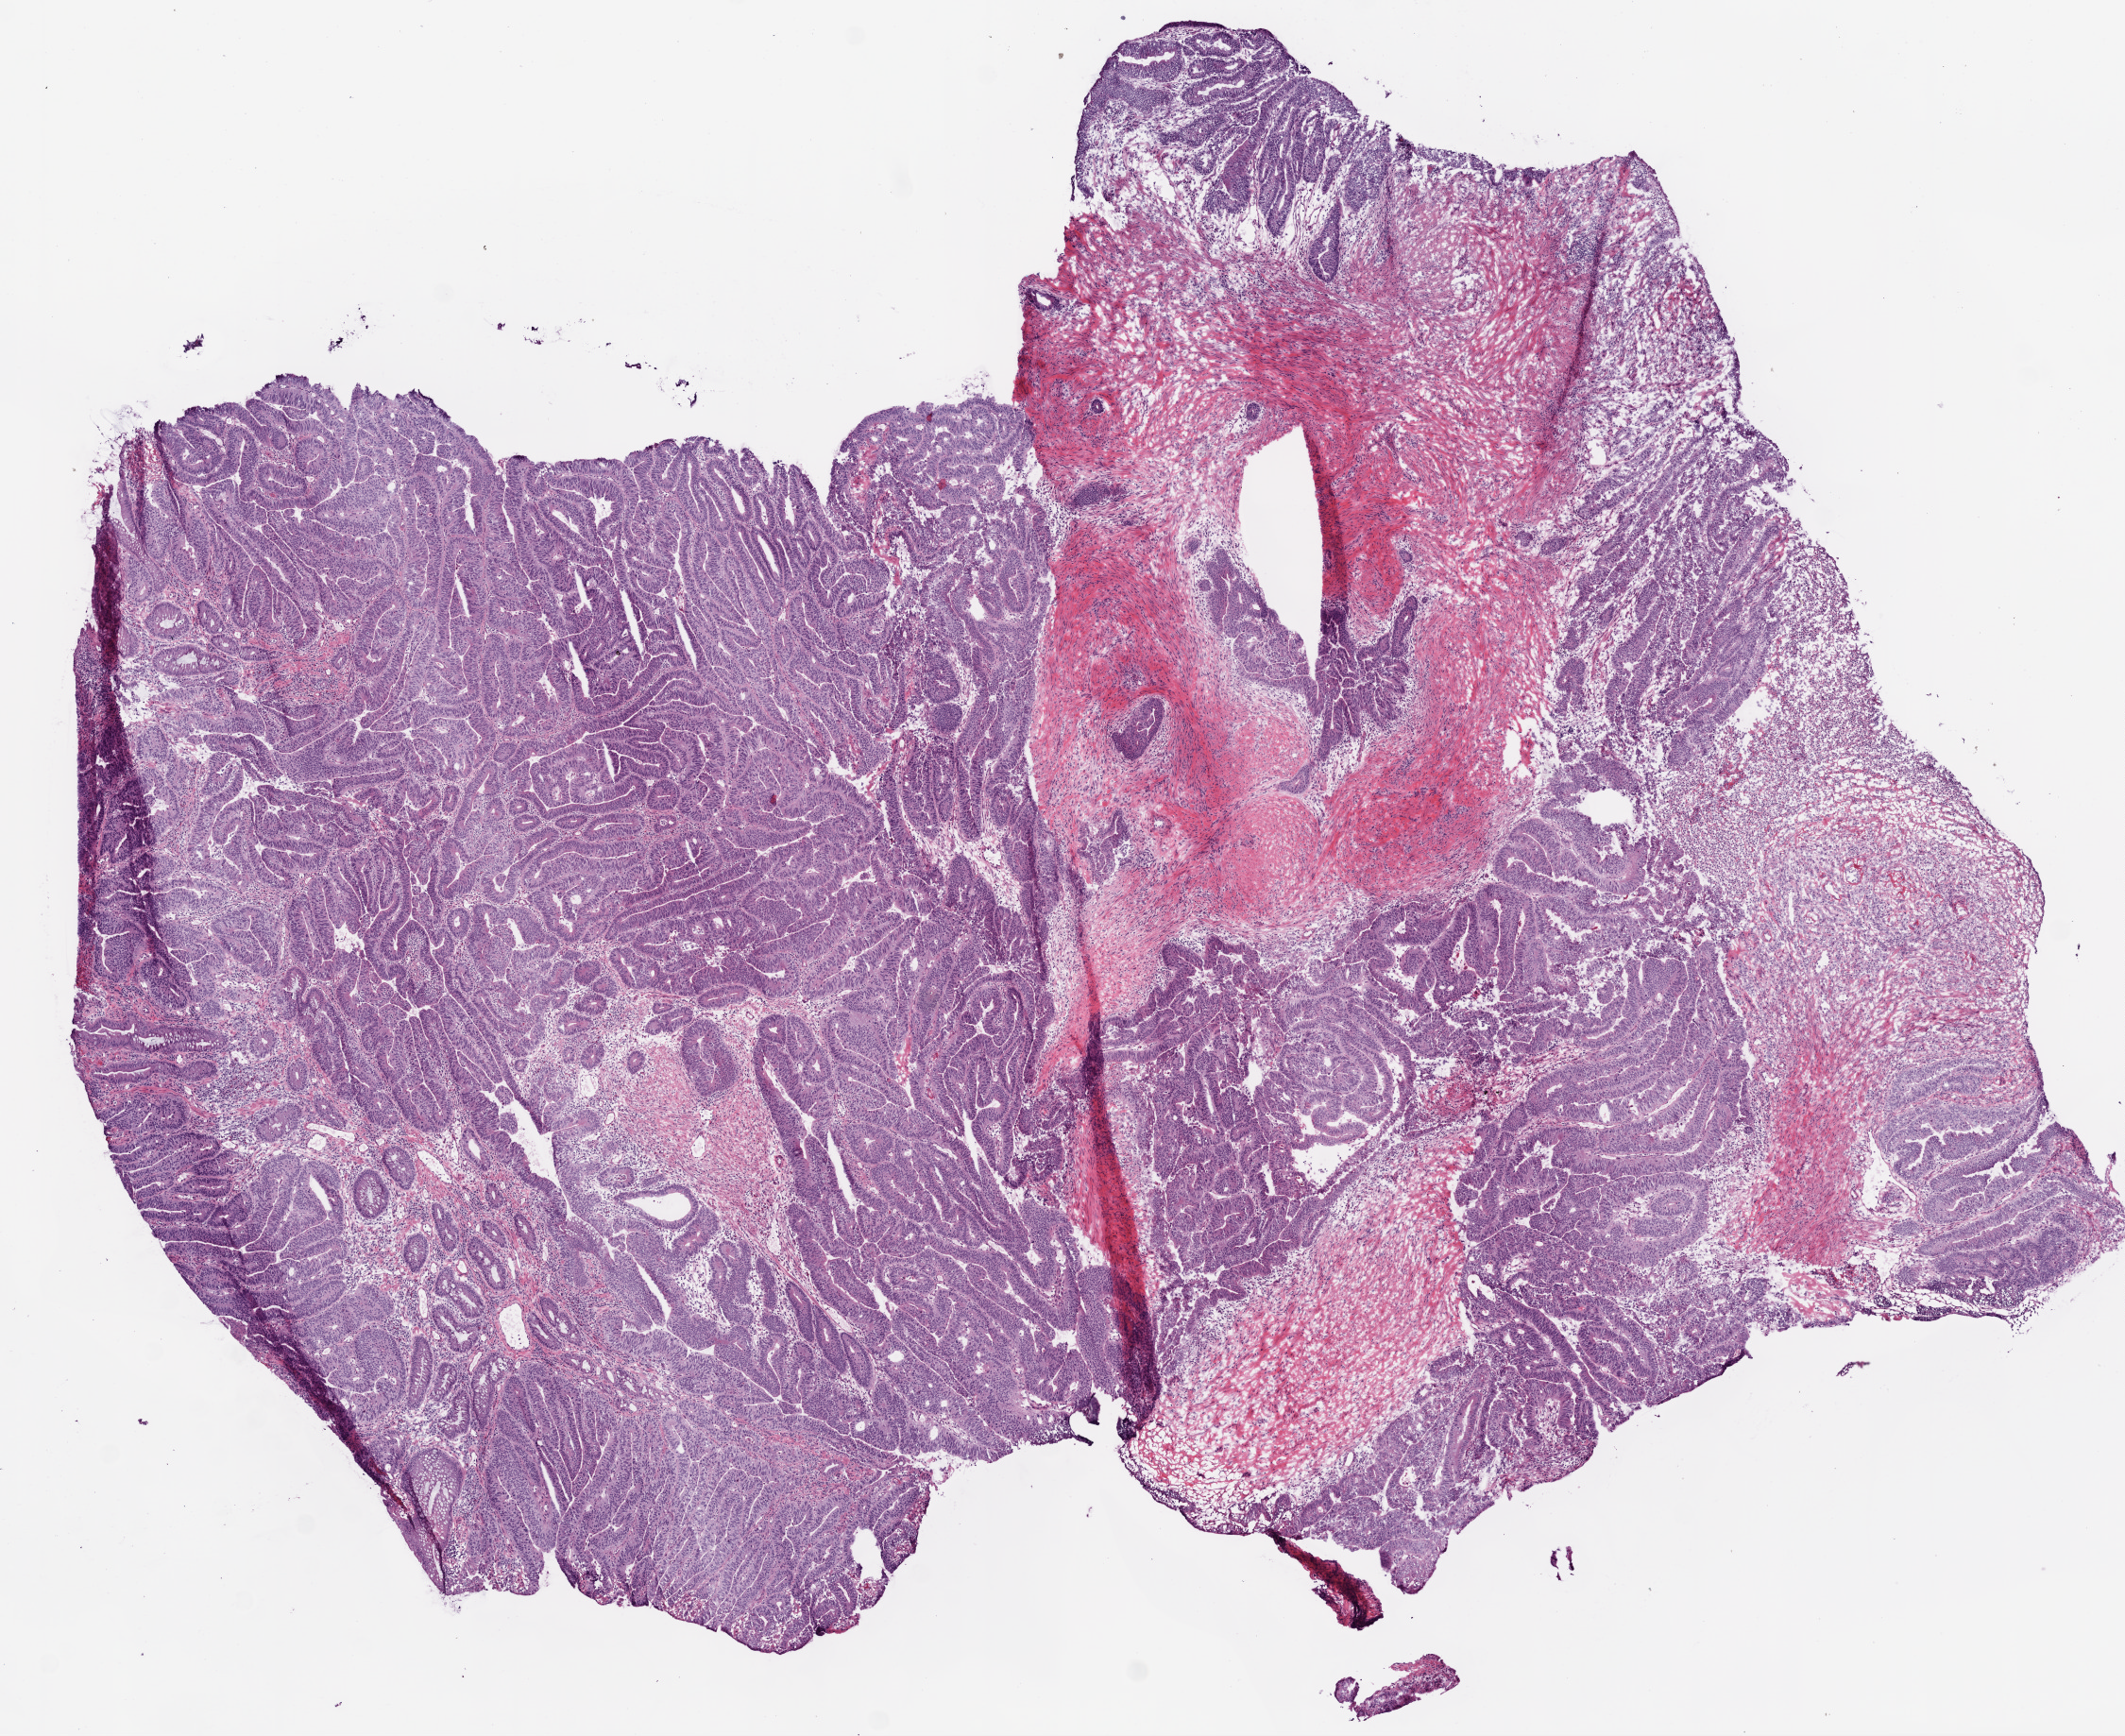
Digitized Hematoxylin and eosin (H&E) stained tissue section (whole slide), shown as a low-resolution overview of the whole scanned area (about 9.0 x 7.4 mm, from a 20x scan); frozen section from the bottom of the tissue portion; sample: primary tumour, colon. Female, age 36 years at initial diagnosis.
Pathologic diagnosis: Adenocarcinoma, NOS.